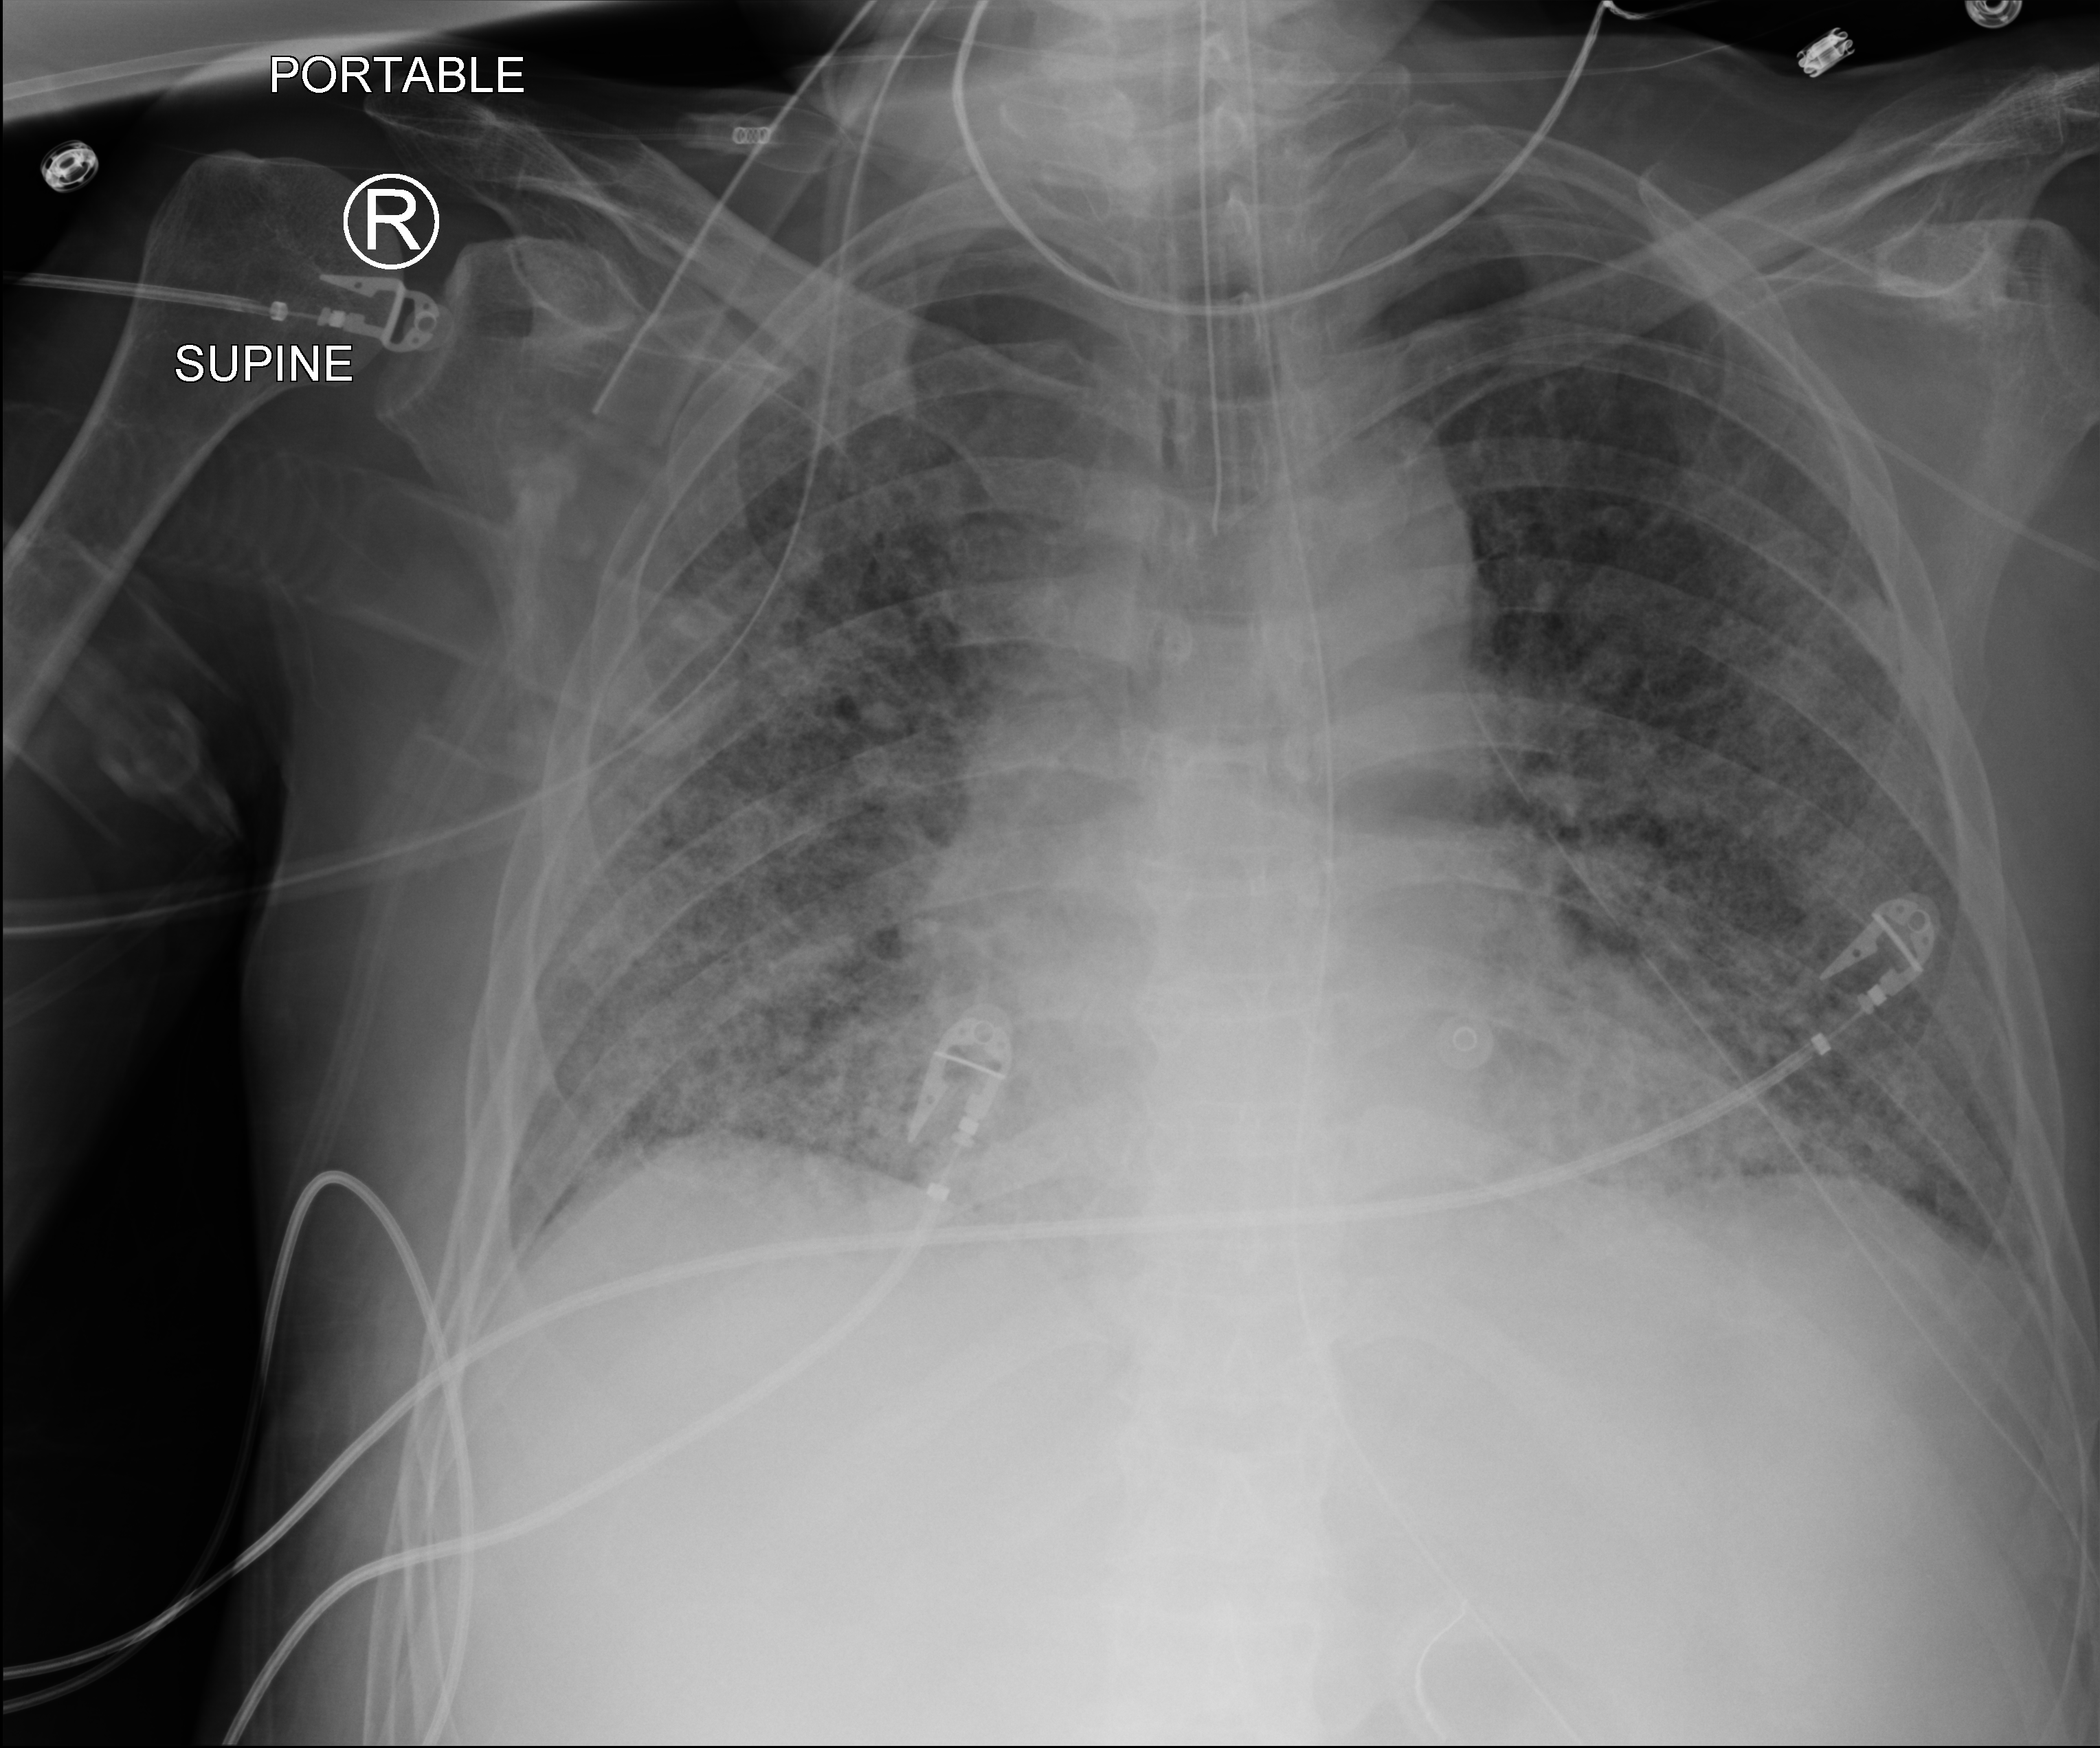
Portable chest radiograph. Patient hospitalised with COVID-19; male, aged 60–74 years.
Admission-level facts for this patient (not findings on this image; timing relative to this image not recorded): admitted to intensive care during this hospital stay: yes; mechanically ventilated during this hospital stay: yes.